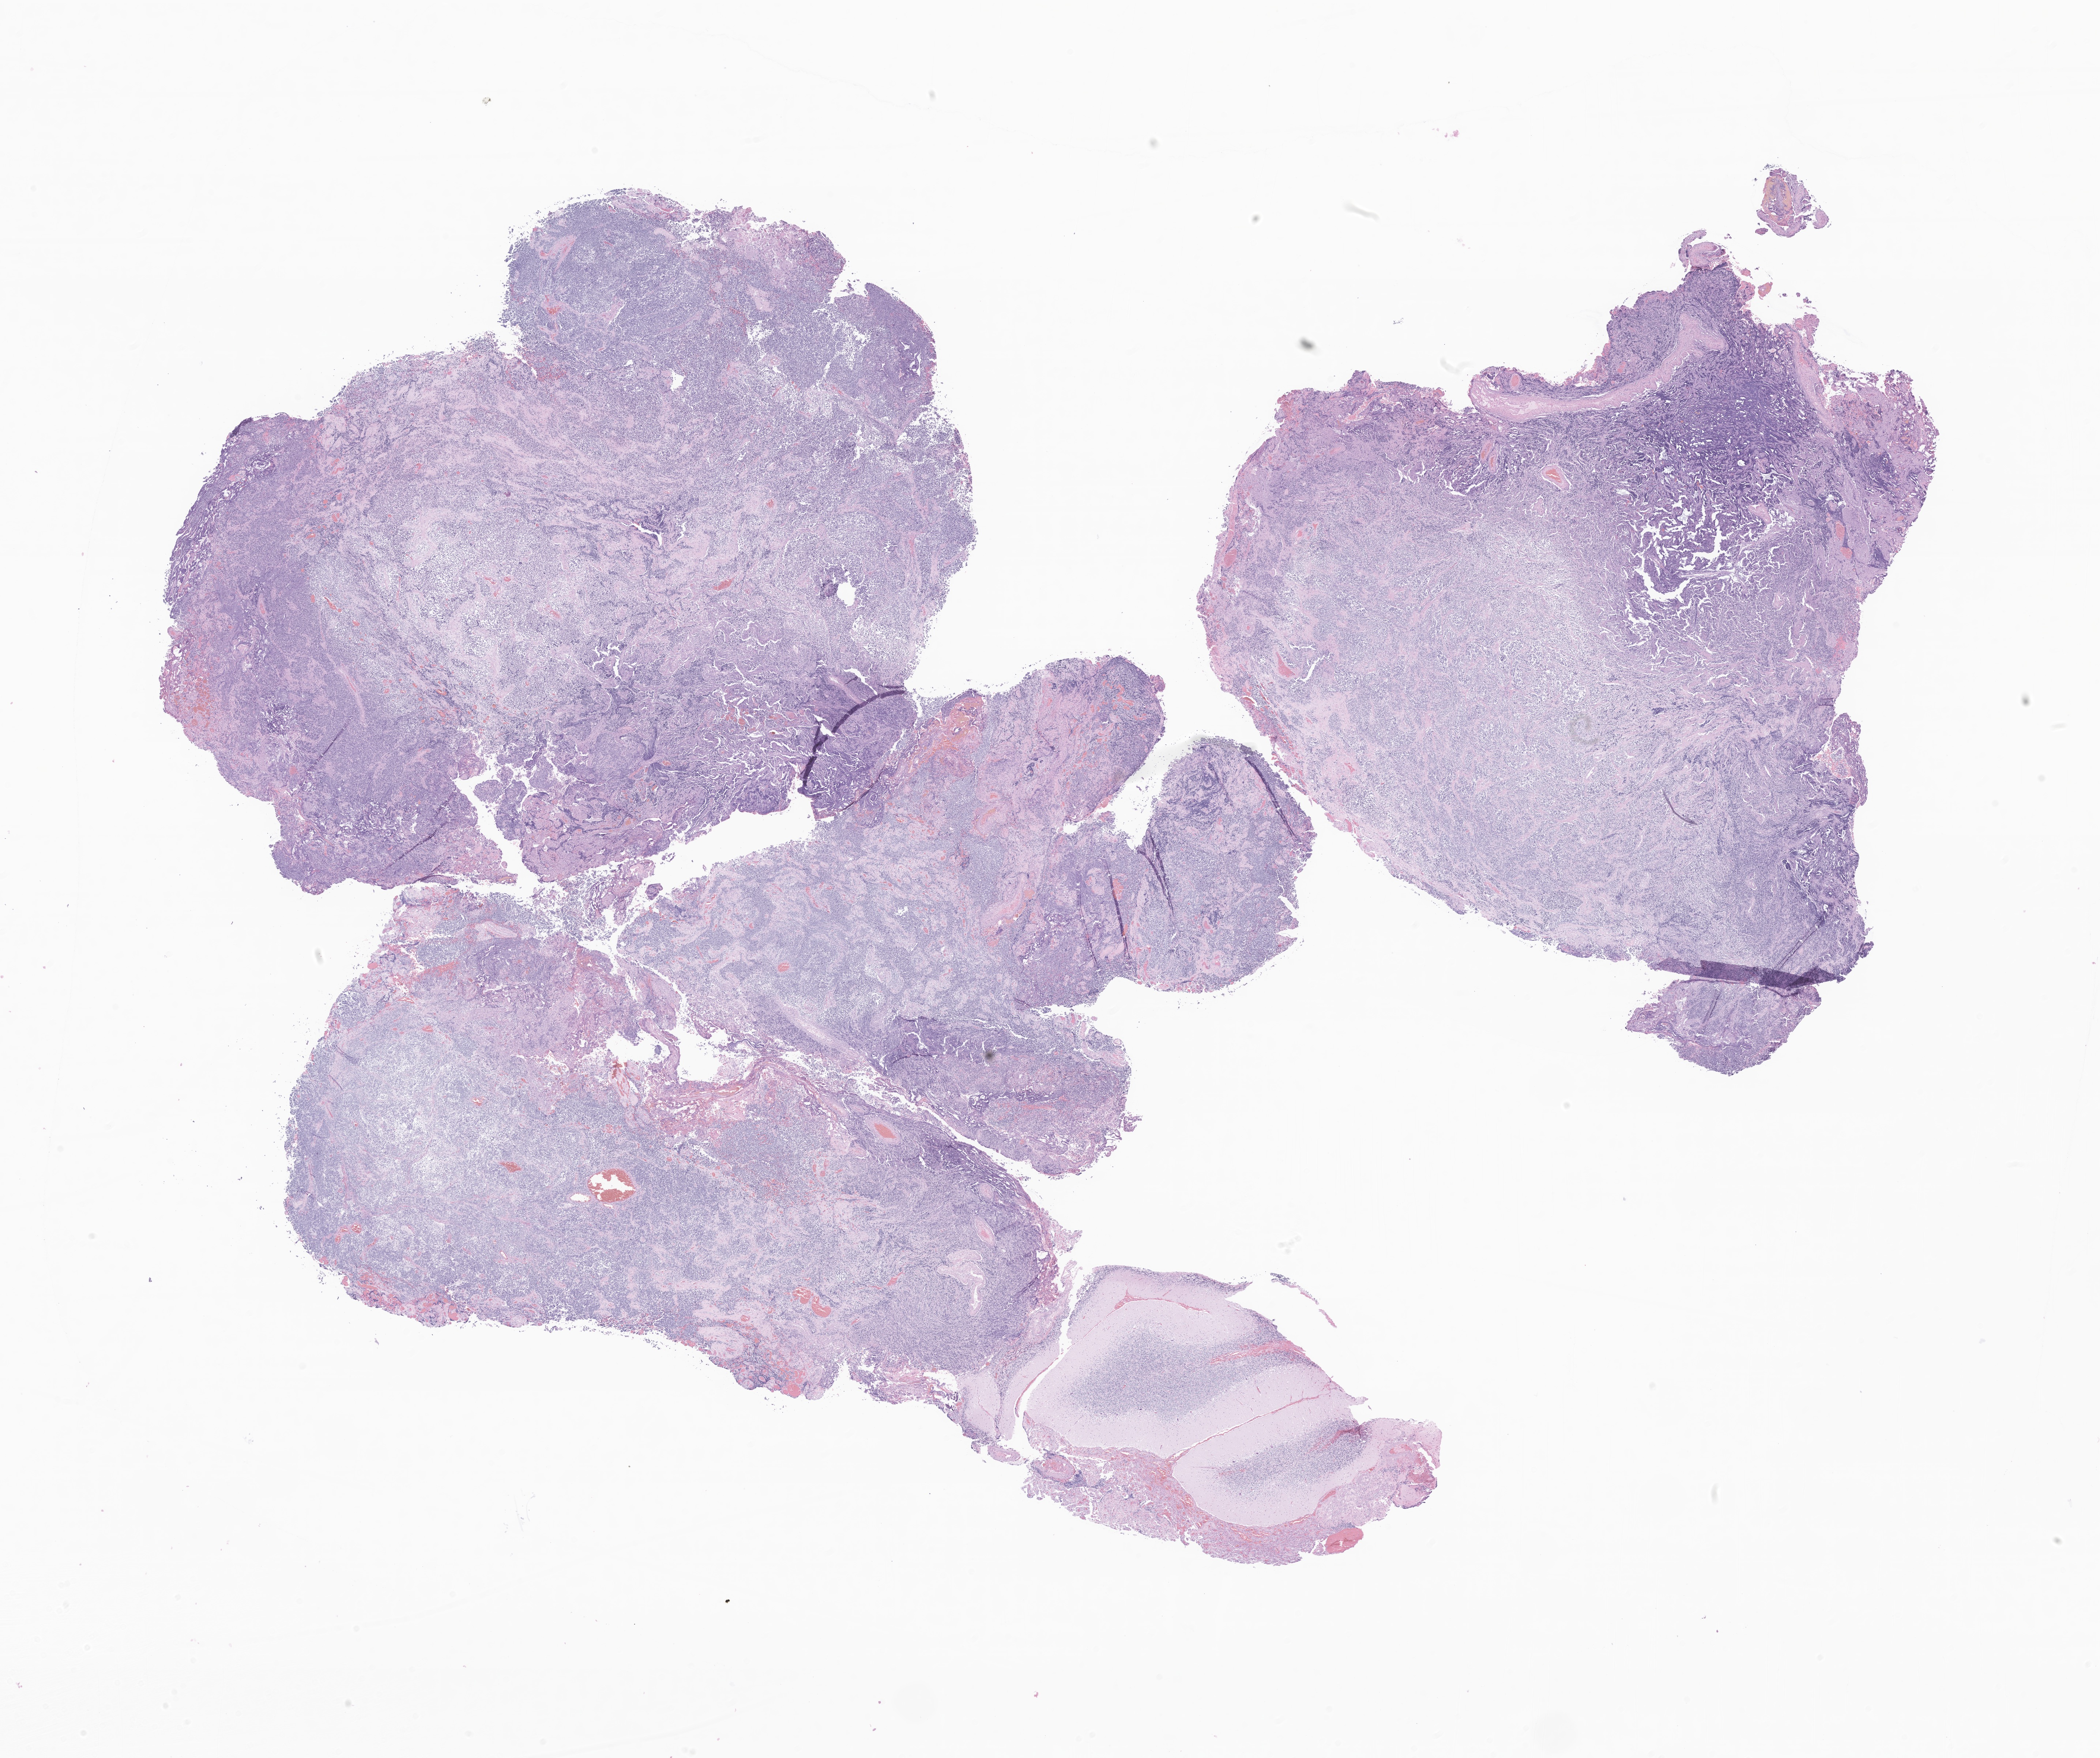
Hematoxylin and eosin (H&E) whole-slide image of tumor tissue from the brain — a low-resolution overview of the entire scanned area, about 24.2 x 20.3 mm; formalin-fixed, paraffin-embedded (FFPE) tissue. Male patient, age 143 months (11 years 11 months).
Recorded diagnosis: Medulloblastoma, NOS.